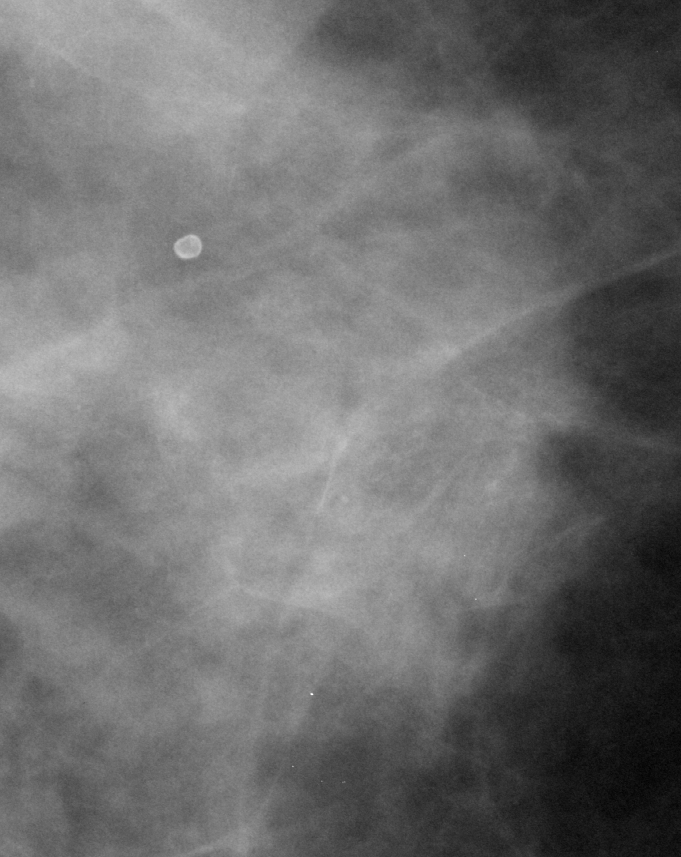
Cropped region of a digitized screen-film mammogram centred on a radiologist-marked abnormality, right breast, CC view.
Calcifications, morphology amorphous, distribution clustered; BI-RADS assessment category 5; subtlety rating 5 on a 1 (subtle) to 5 (obvious) scale; pathology result (as recorded, not read from the image): malignant.